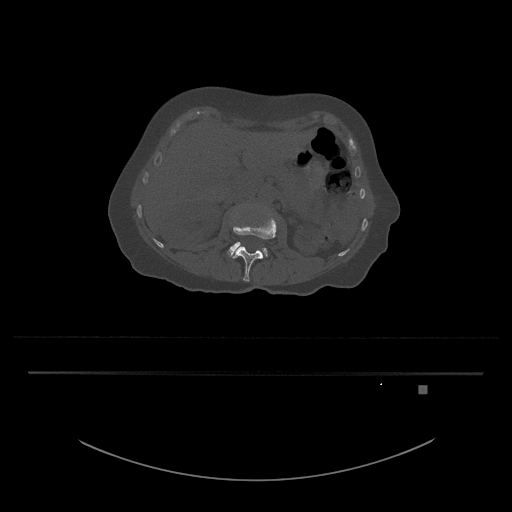
CT including the spine, one axial slice. Slice 474 of 797 in the series (ordered by position). Reconstruction kernel Br40s/3. 120 kVp. Bone window (W 1800 / L 400 HU). 512 × 512 image matrix, field of view 500 × 500 mm. Patient: female, 57 years. Case-level facts recorded for this patient, not image findings: primary cancer: cervical.
Outlined on this slice (semi-automatically segmented with operator editing):
- L3 vertebra: bounding box <227,242,268,258> (left, top, right, bottom; pixels)